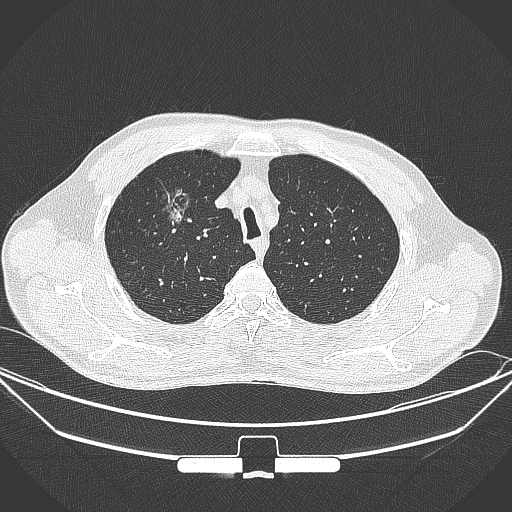
Chest CT, one axial slice; slice 280 of 355 in the series (ordered by position); 120 kVp; lung window (W 1500 / L -600 HU); 1 mm slice thickness; 512 × 512 image matrix. Male patient, age 67 years. Case-level facts recorded for this patient, not image findings: clinical TNM (as recorded): T1c N0 M0.
Annotated regions visible in this slice (rectangle marked by the reading radiologist):
- lung tumour (recorded histology: adenocarcinoma): bounding box (x1, y1, x2, y2) in pixels: (146, 174, 193, 235)